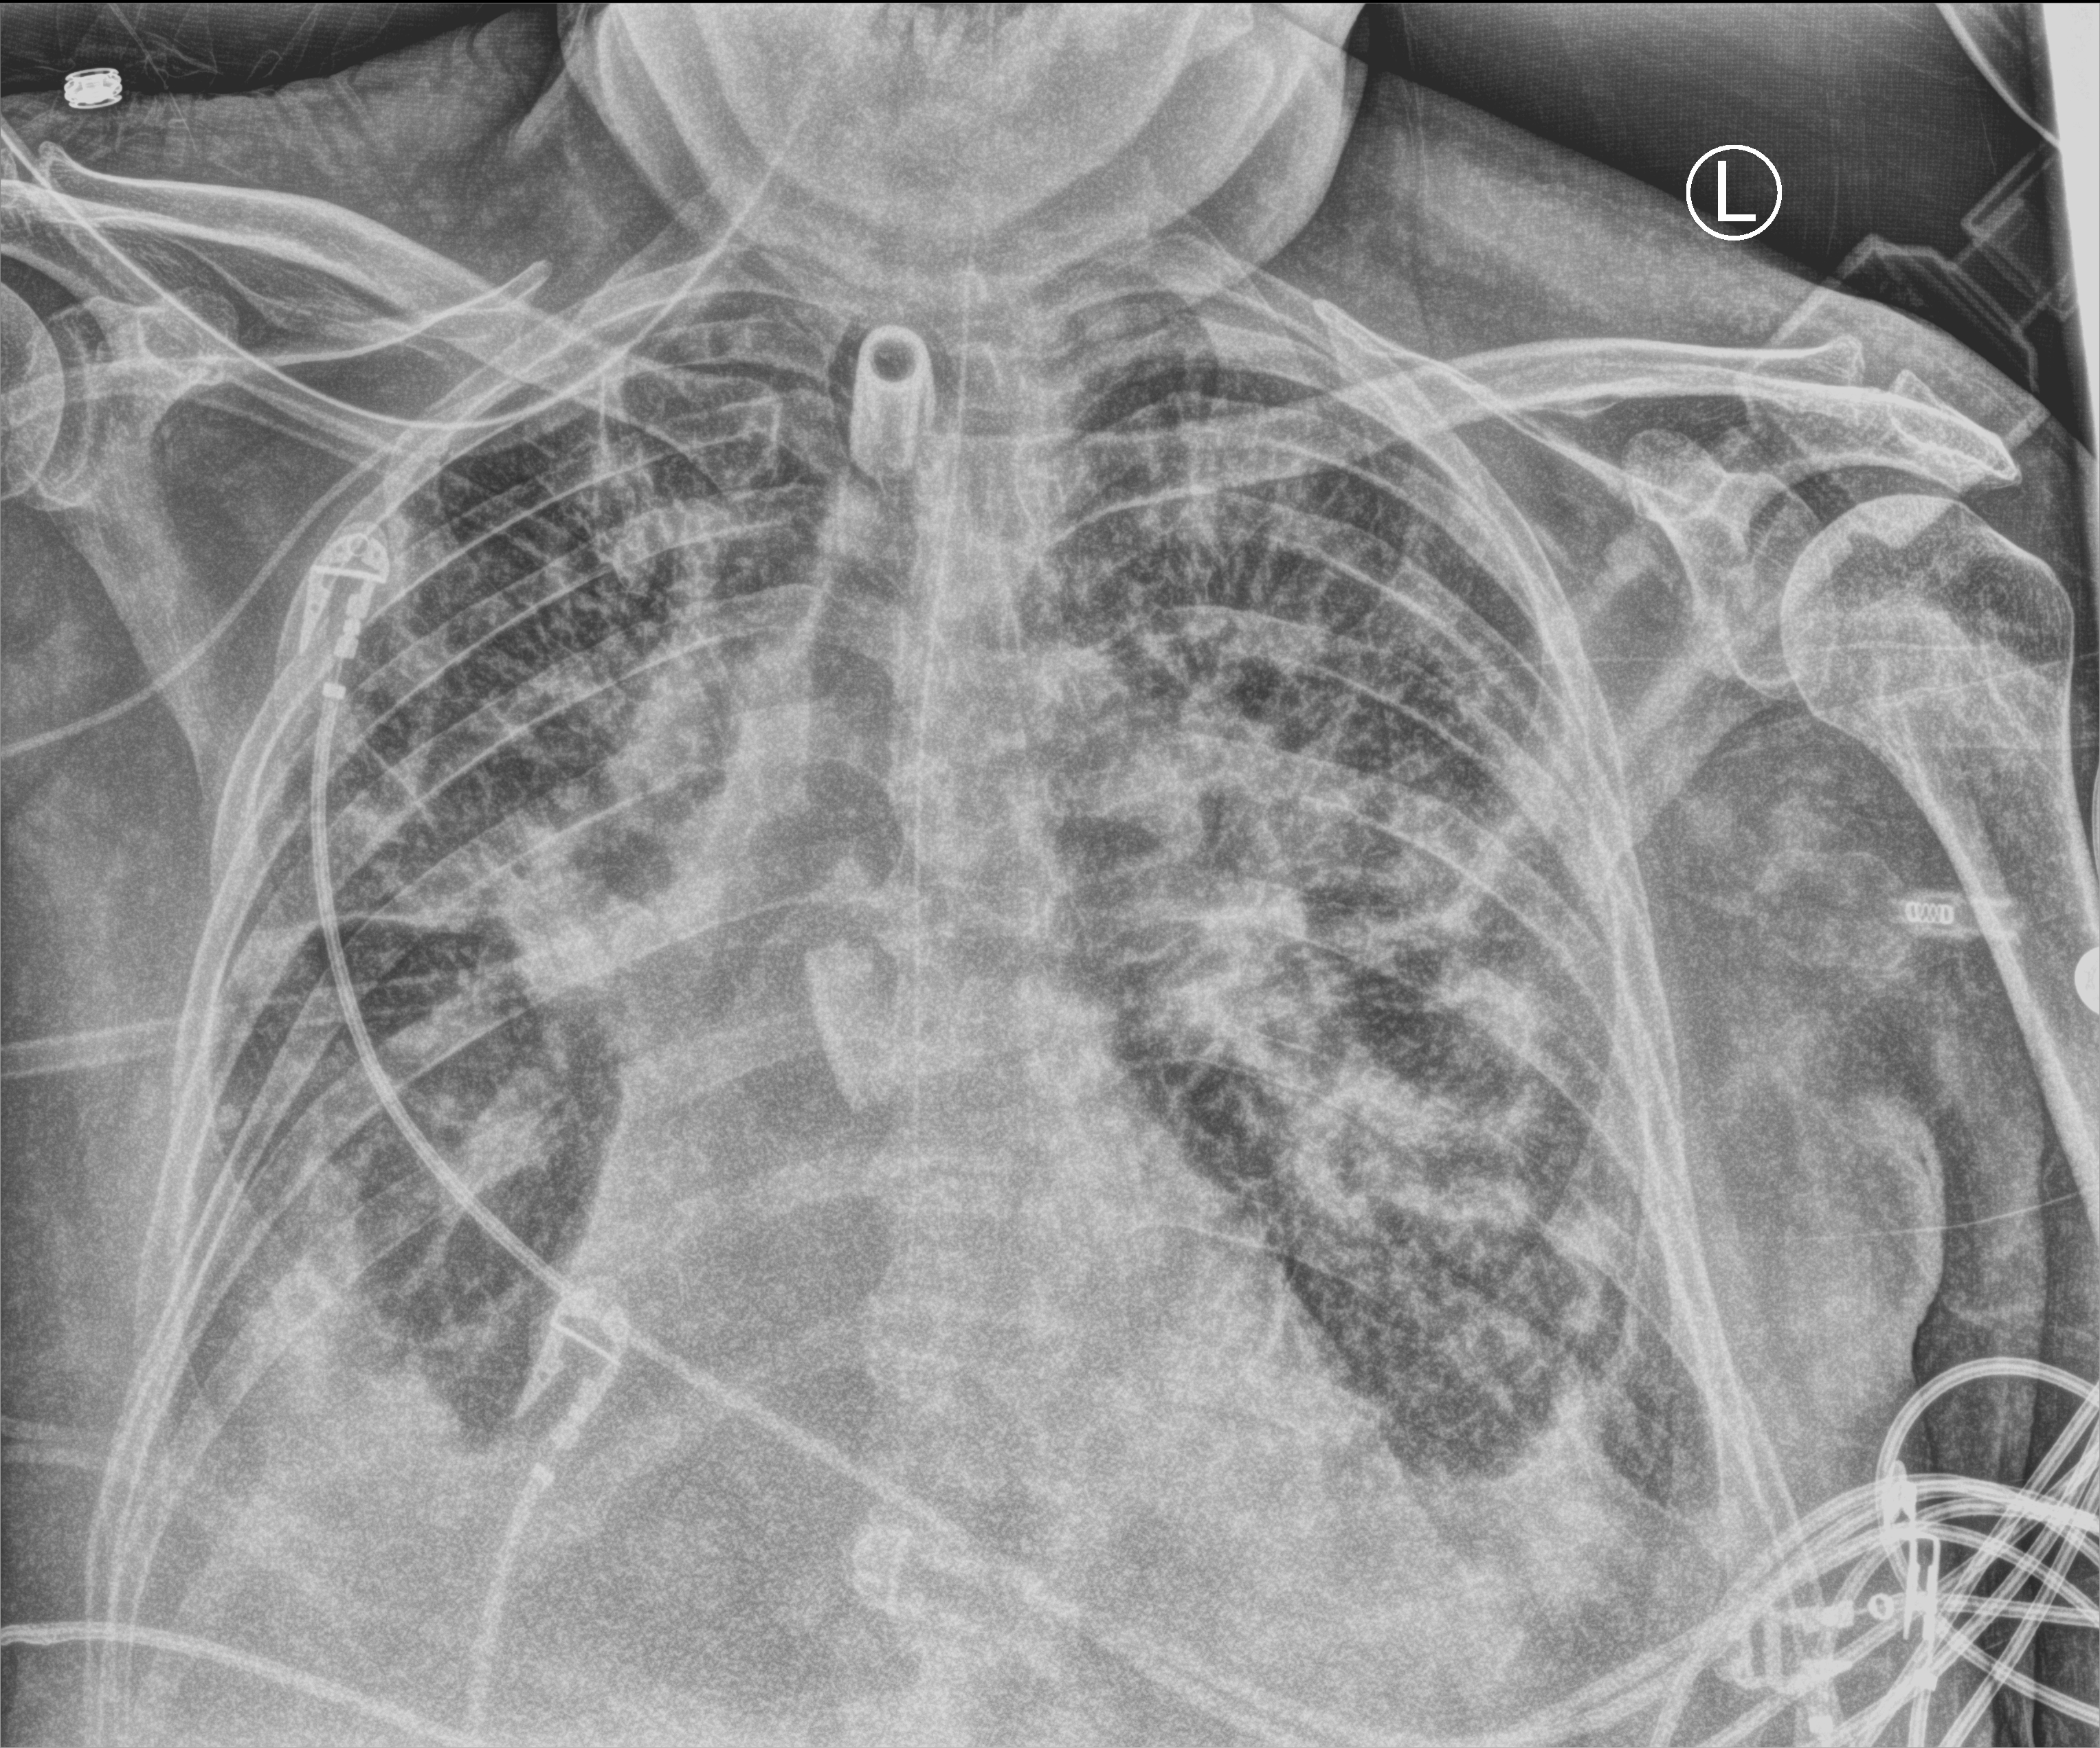
Portable chest radiograph. Patient hospitalised with COVID-19; male, aged 75–90 years.
Admission-level facts for this patient (not findings on this image; timing relative to this image not recorded):
- admitted to intensive care during this hospital stay: yes
- other chronic lung disease (admission record): yes
- mechanically ventilated during this hospital stay: yes